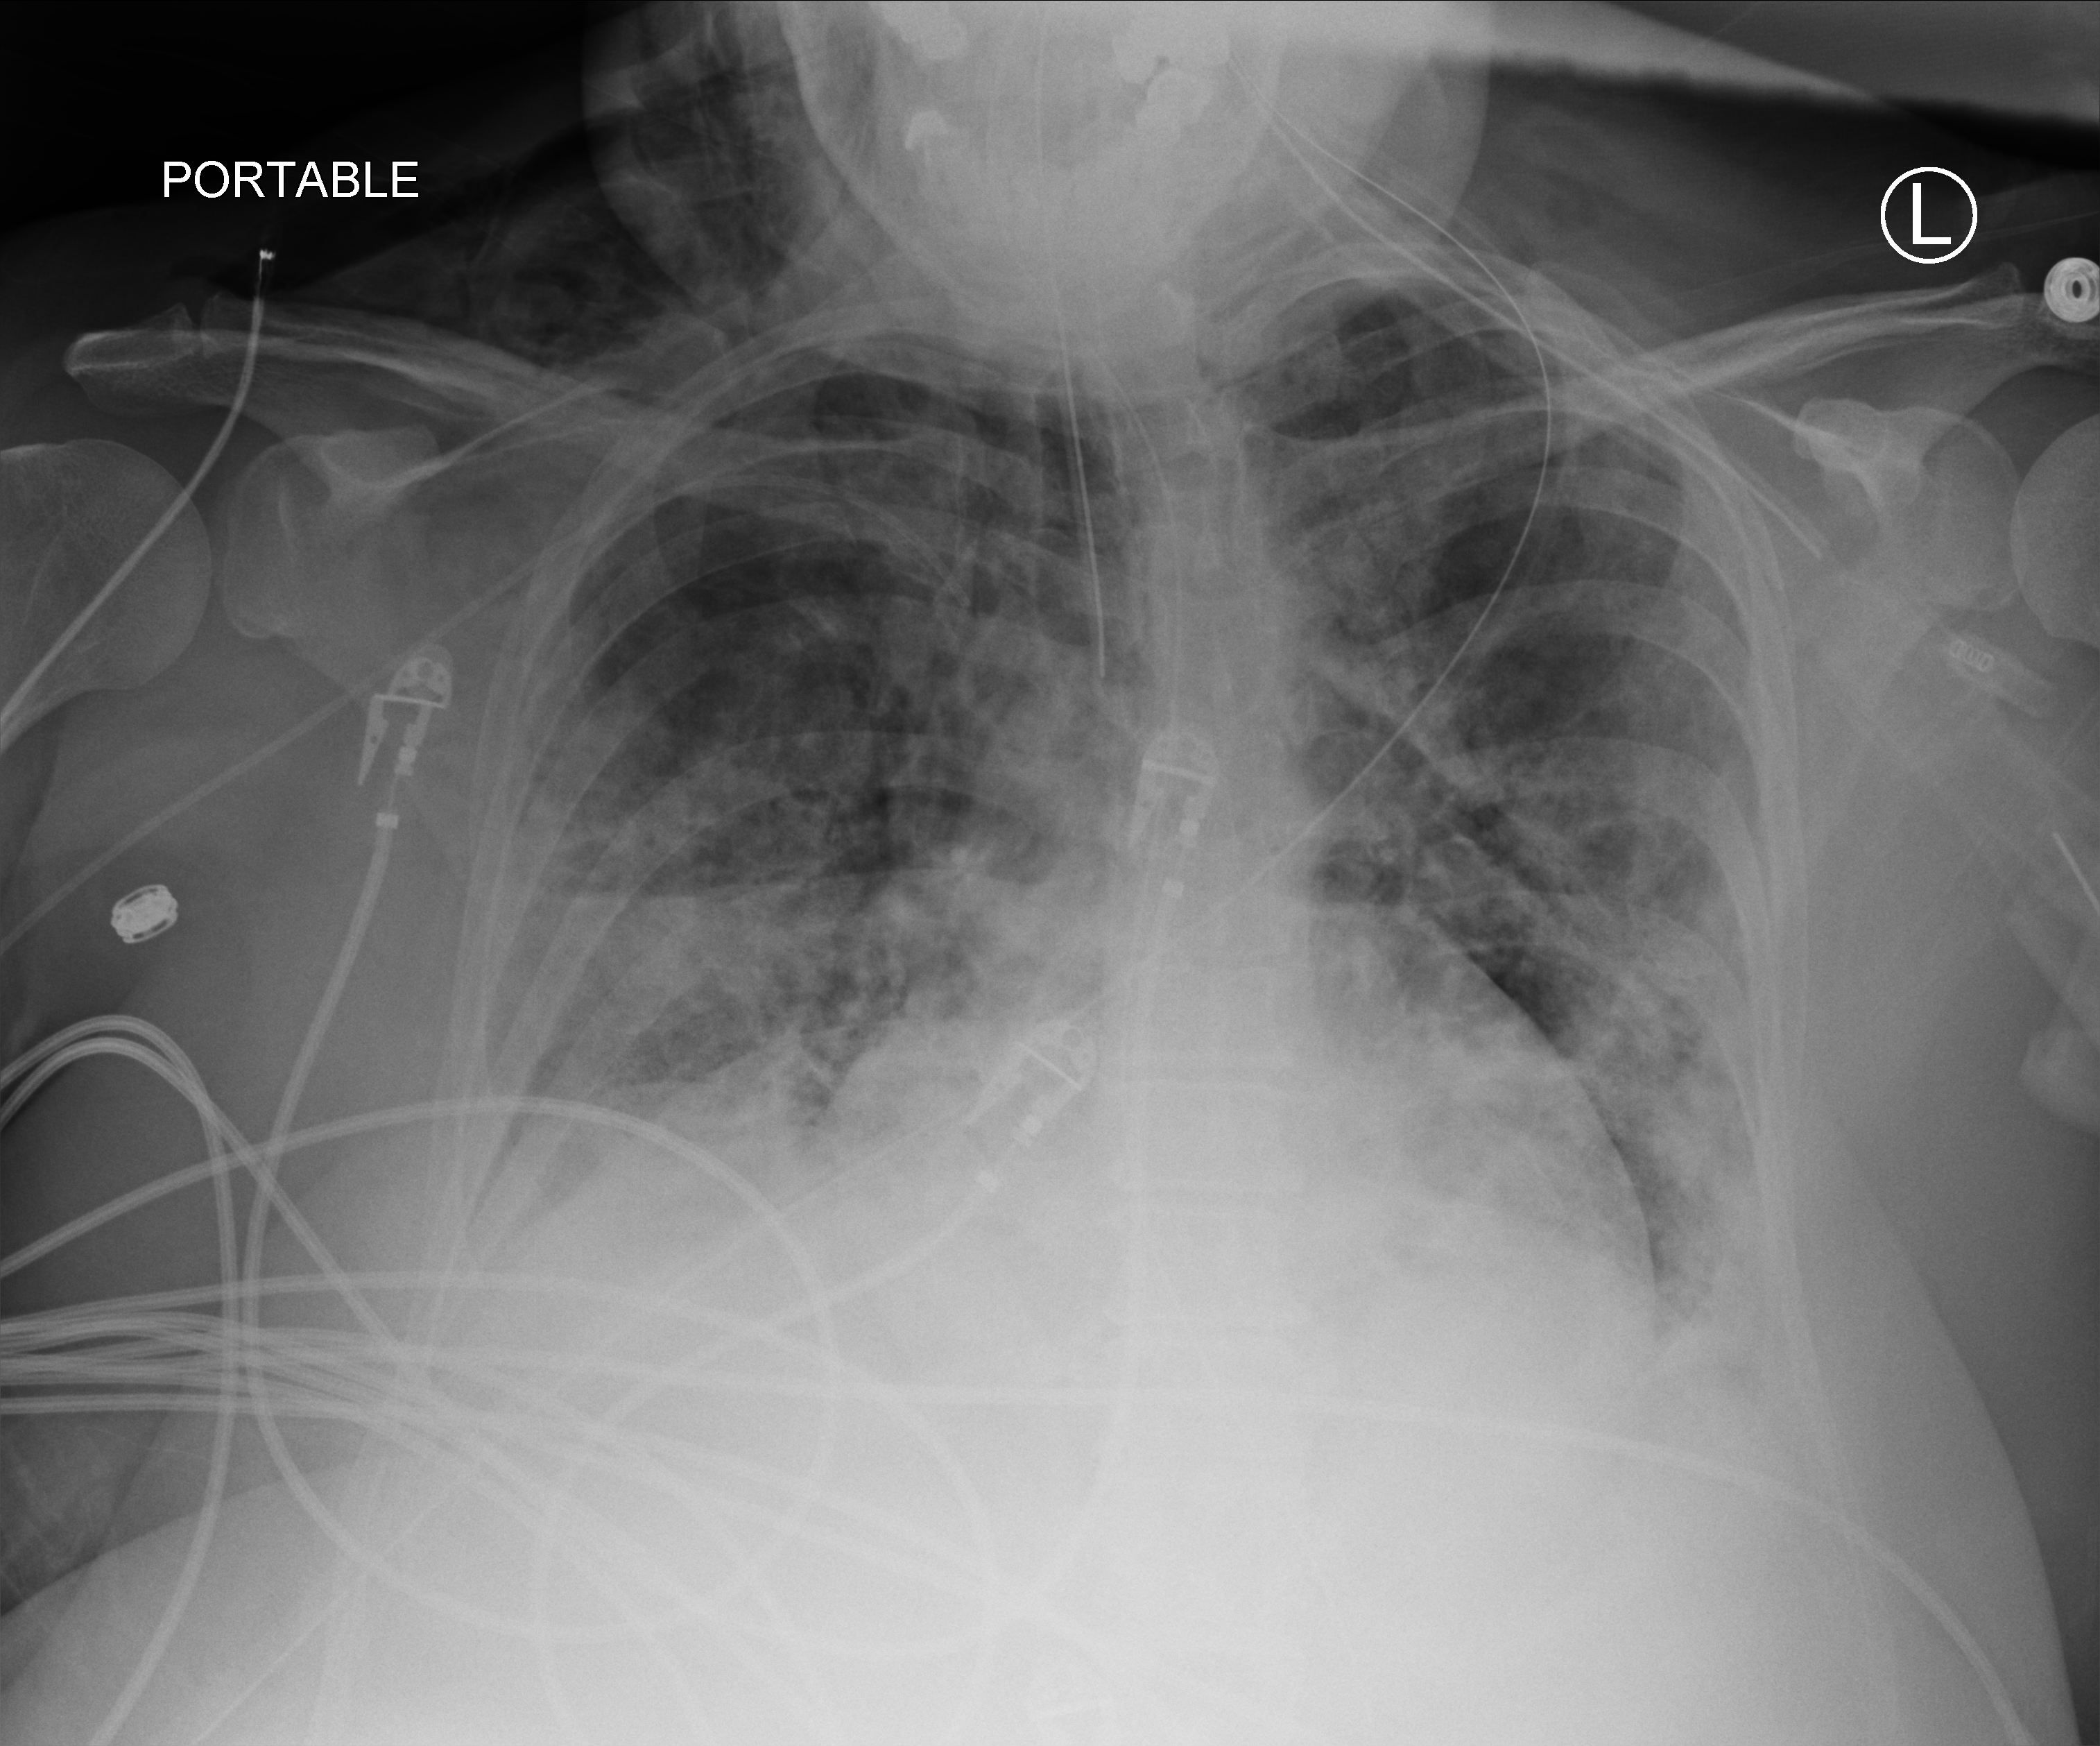
Portable chest radiograph; anteroposterior (AP) projection. Female patient hospitalised with COVID-19, age 60–74 years.
Admission-level facts for this patient (not findings on this image; timing relative to this image not recorded): mechanically ventilated during this hospital stay: yes.